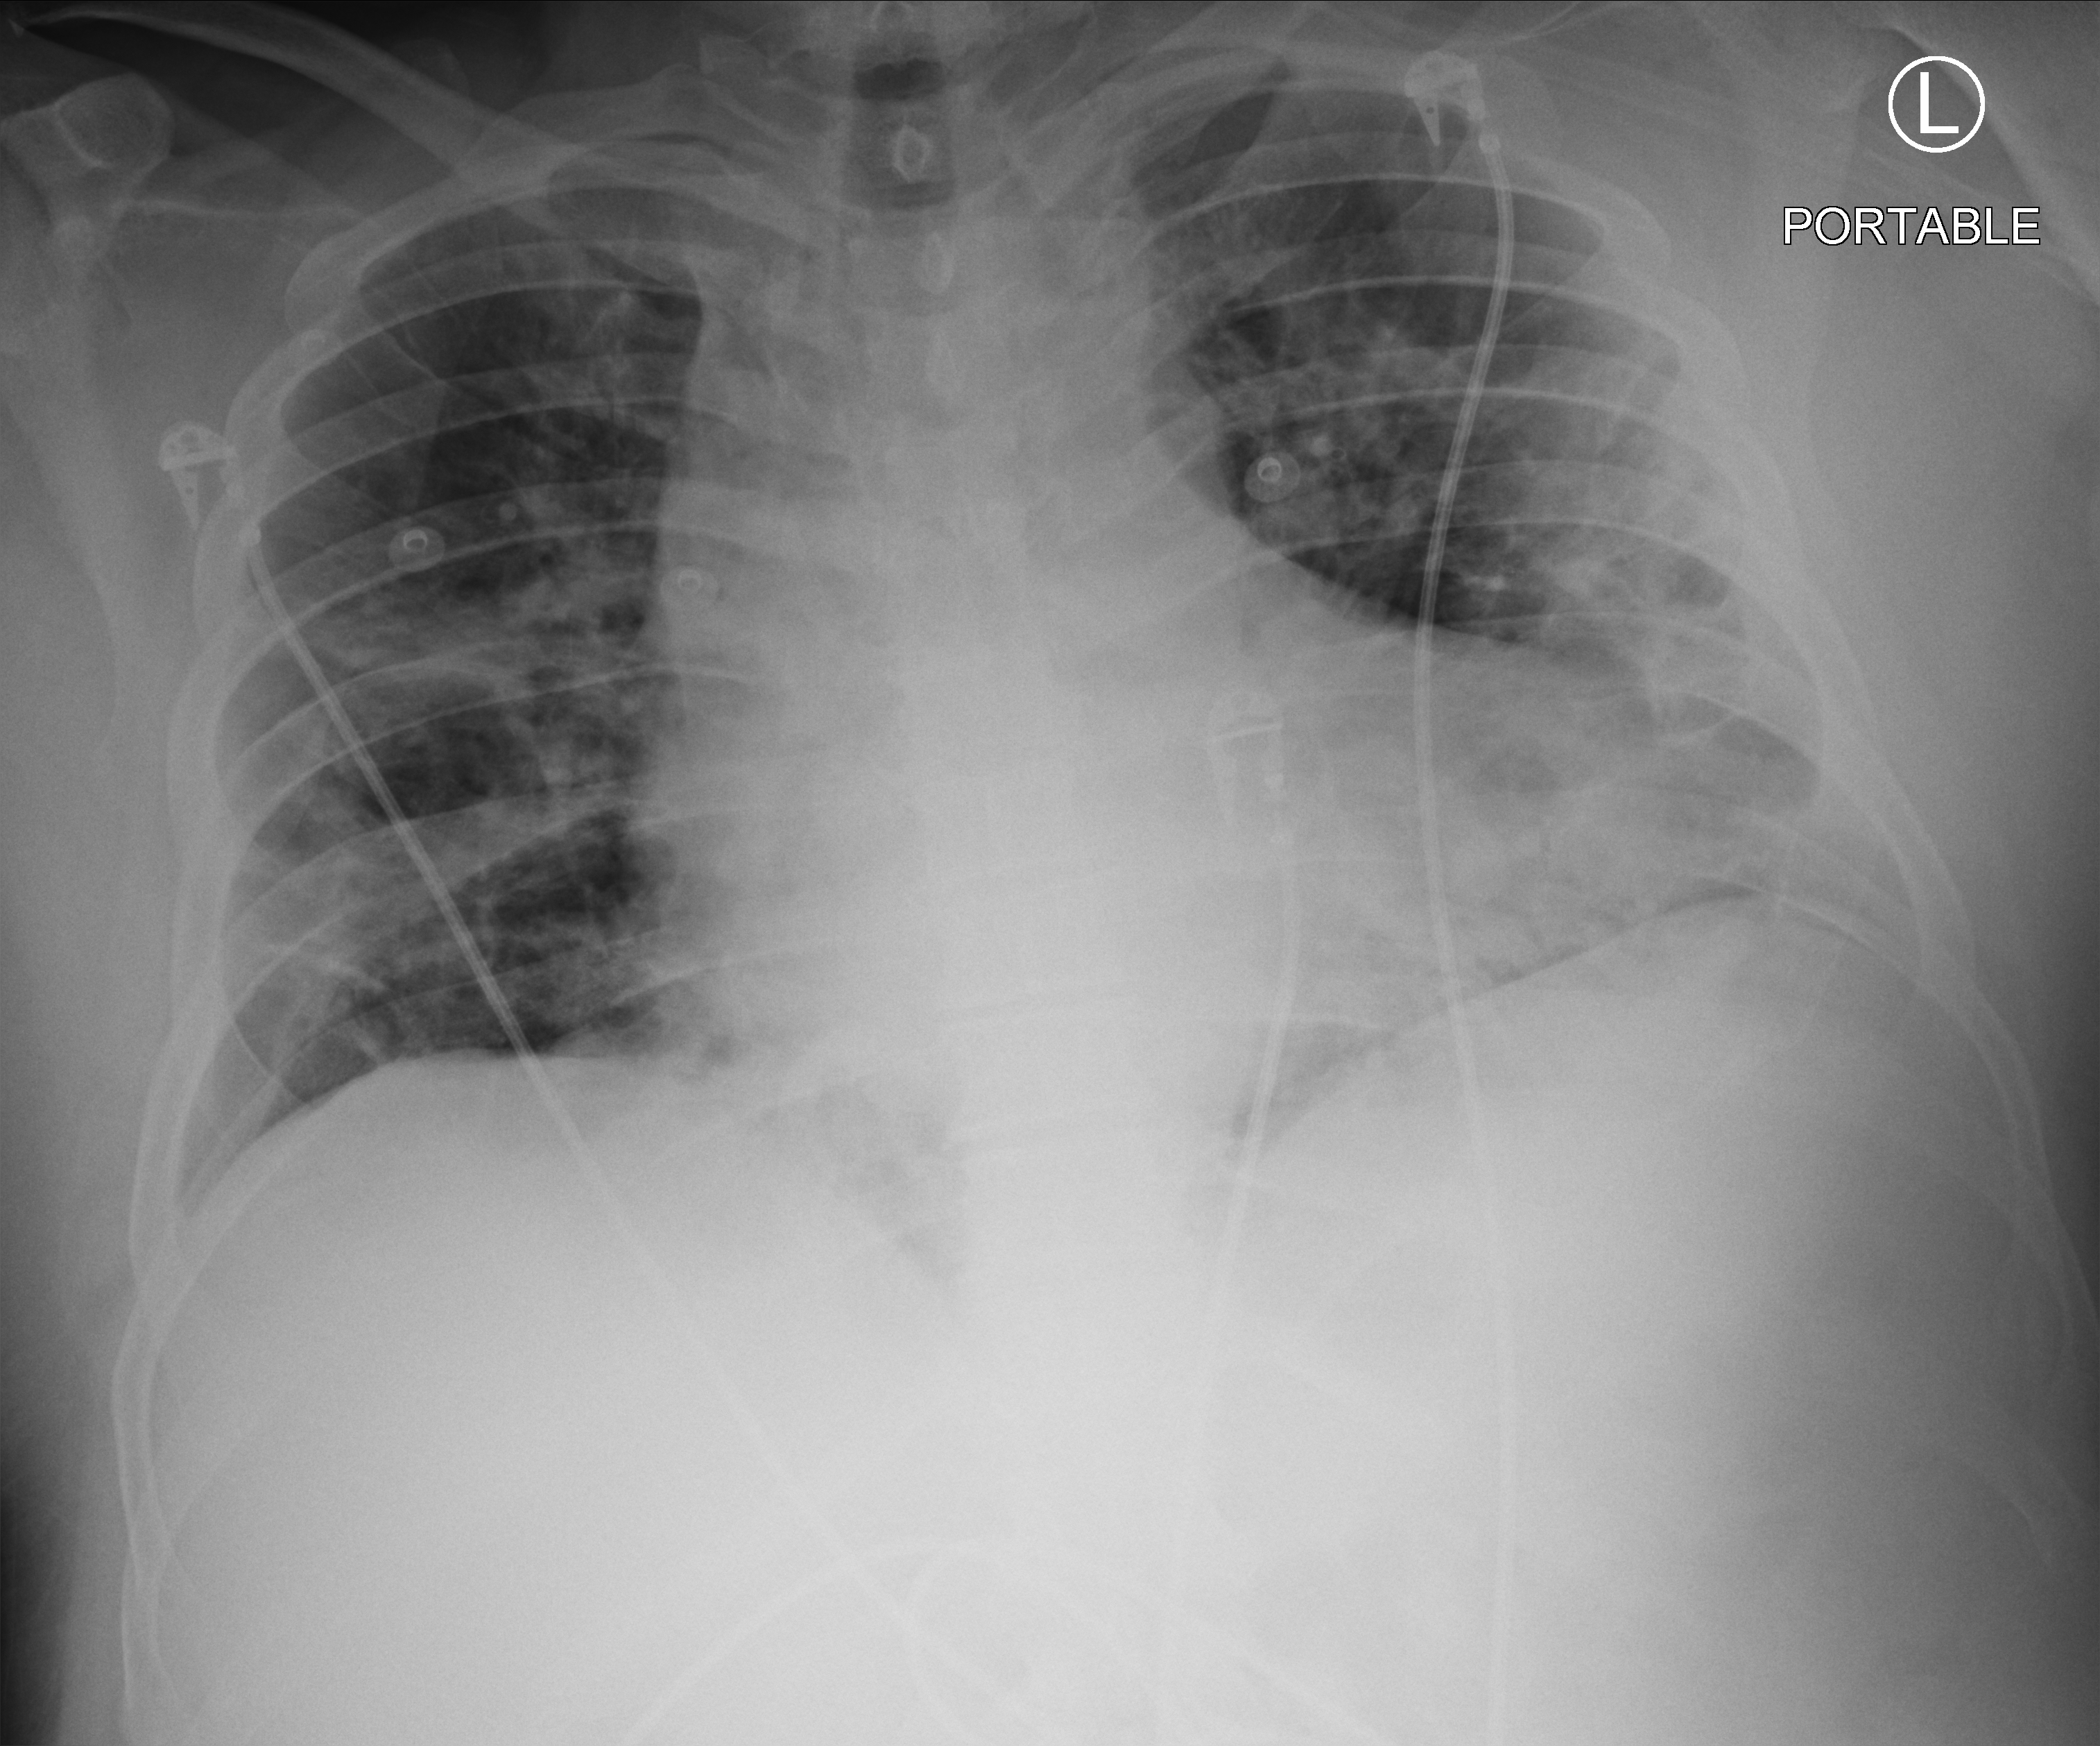
Chest X-ray (portable), anteroposterior (AP) projection. Male patient hospitalised with COVID-19, age 18–59 years.
From the hospital-stay record, not from the radiograph (when in the stay this image was taken is not recorded):
- hypertension (admission record): no